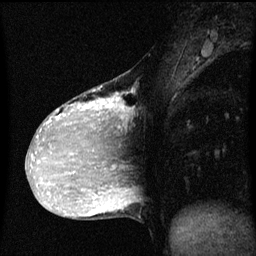
Breast MRI (dynamic contrast-enhanced), one sagittal slice; position 26 of 60 along the scan axis; dynamic contrast-enhanced series, image 2 of 3 at this slice position (ordered by acquisition); 1.5 T; TE 4.2 ms, TR 8 ms; 2 mm slice thickness; 256 × 256 image matrix, field of view 200 × 200 mm. Patient: female, 36 years.
Outlined on this slice (semi-automatically segmented with operator editing):
- analysis volume of interest (the breast-tissue region the enhancement analysis was run in; not a lesion): bounding box [x1, y1, x2, y2] px = [33, 72, 130, 169]
- tumour enhancement mask (voxels above the 70 % enhancement threshold inside the analysis volume of interest): [38, 86, 129, 169]